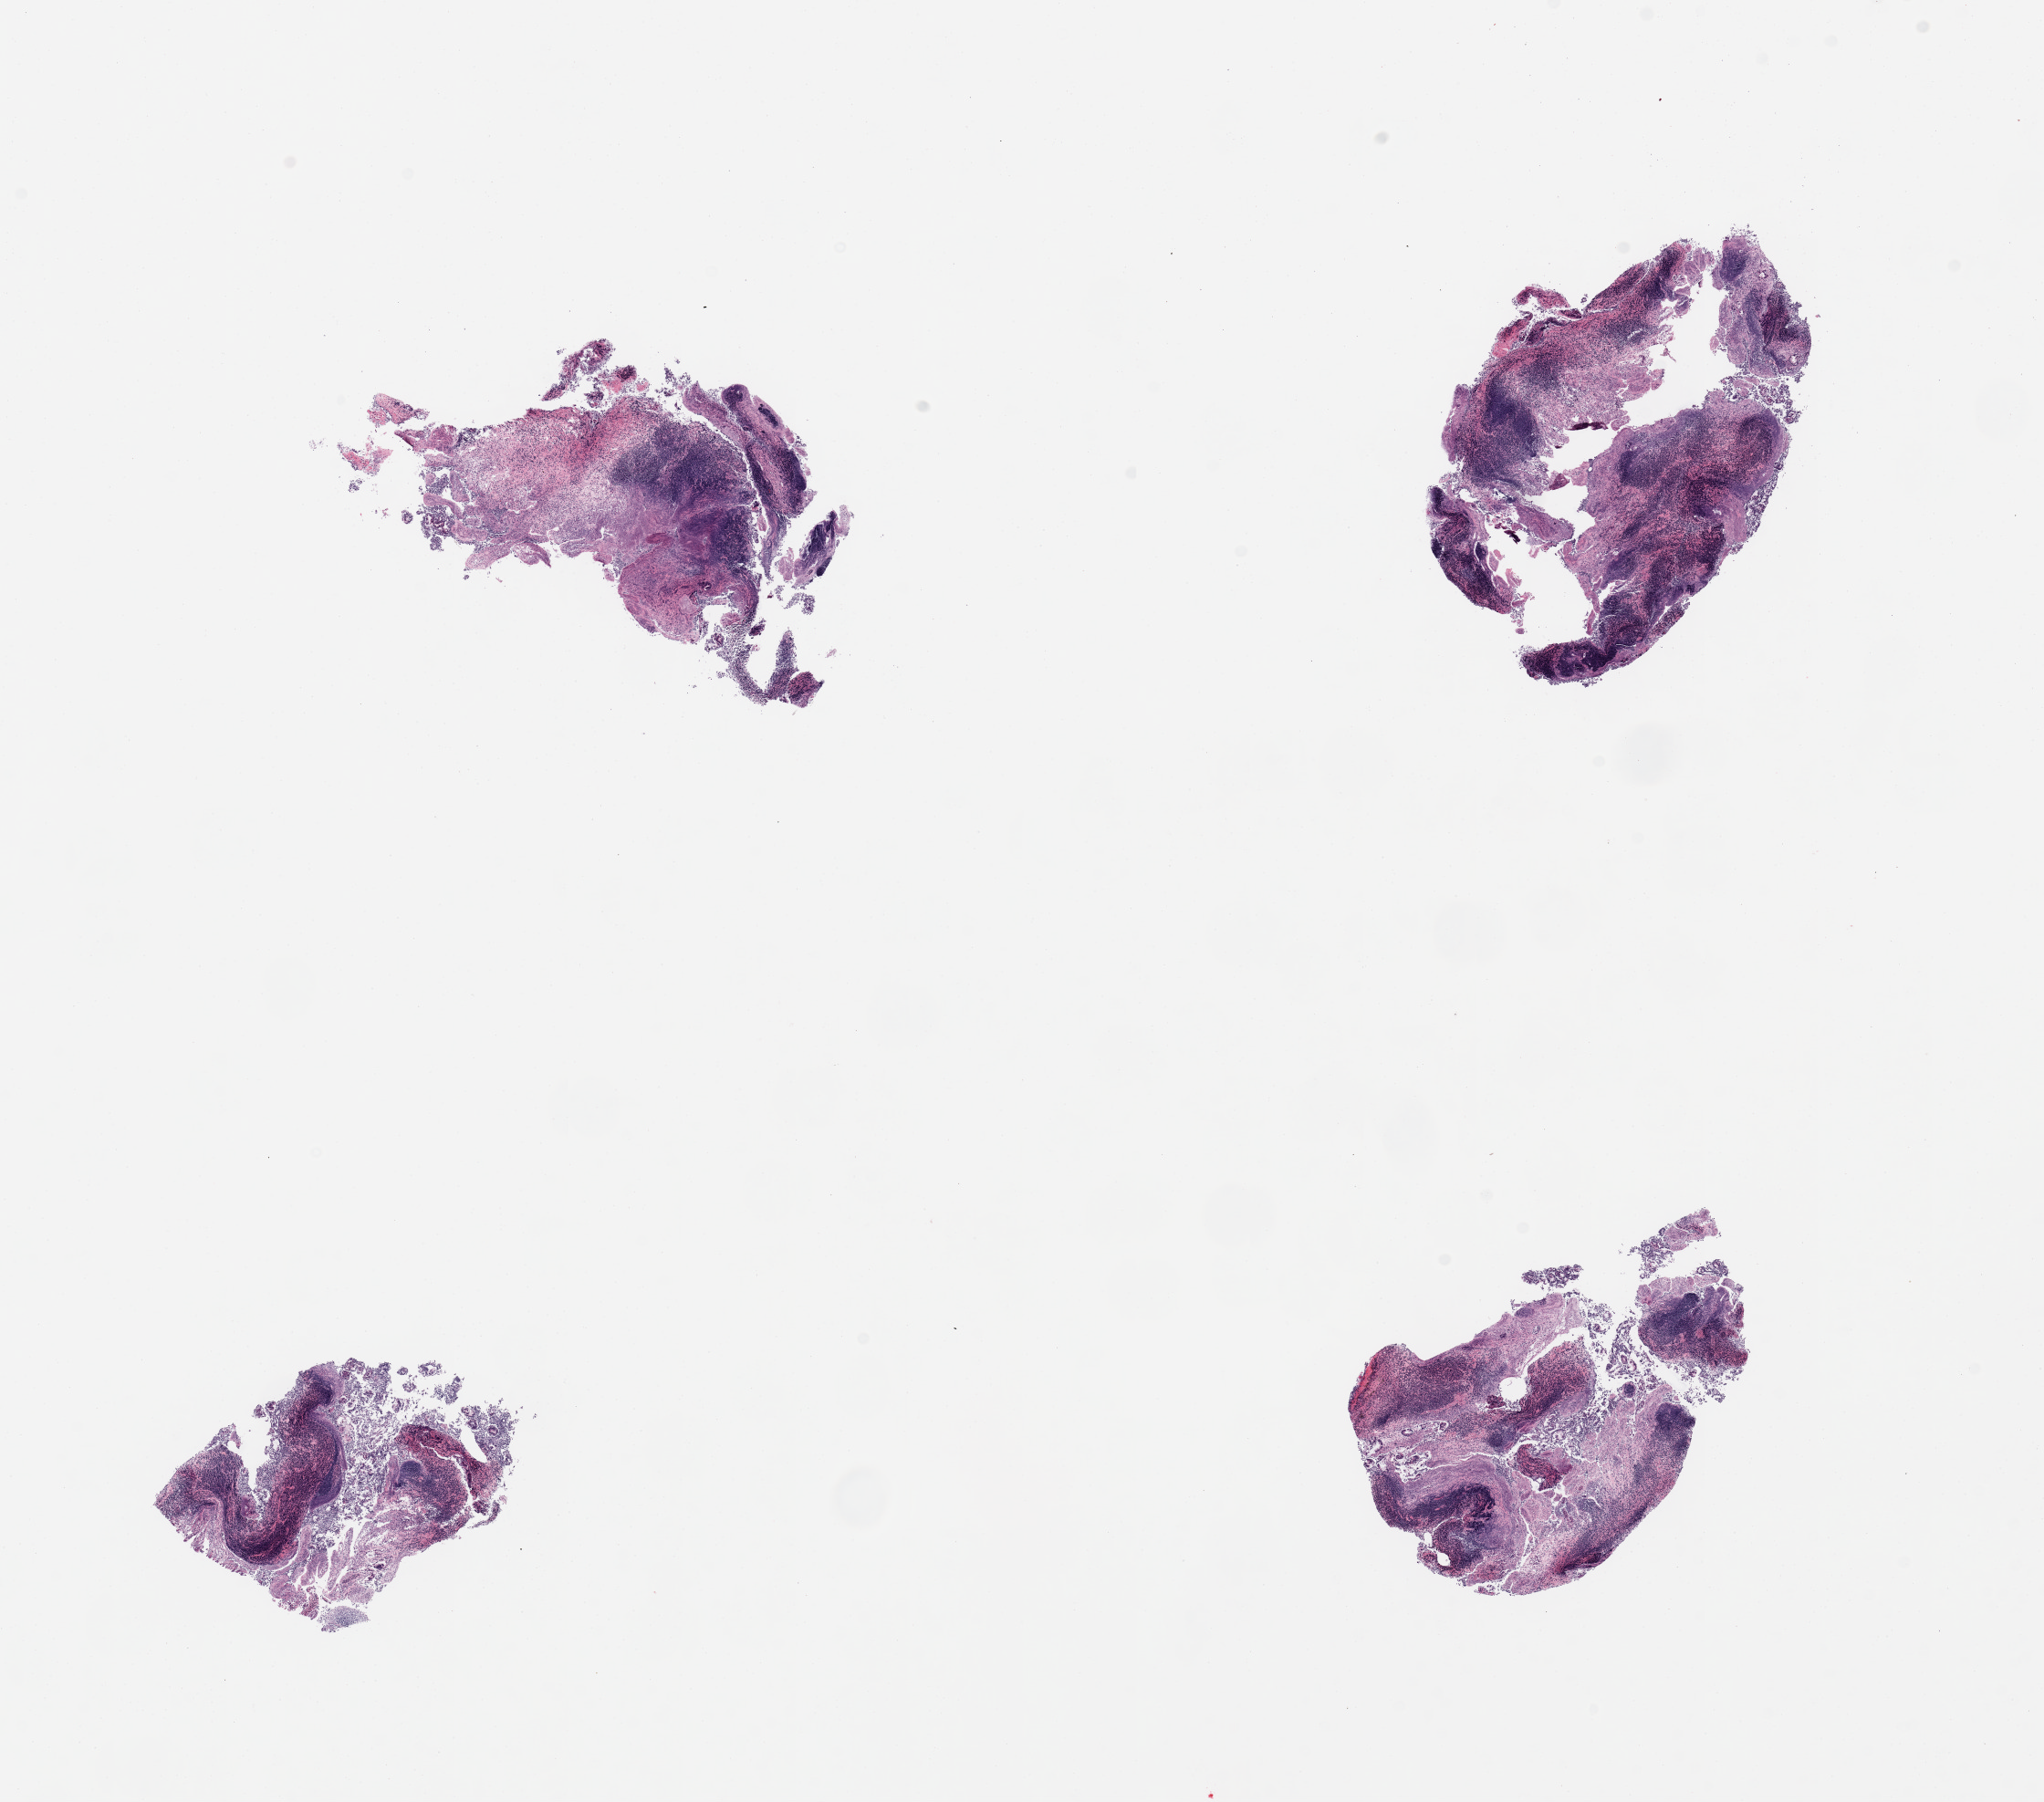
Digitized haematoxylin and eosin-stained section — a low-resolution overview of the entire scanned area, about 17.7 x 15.6 mm; PAXgene-fixed, paraffin-embedded tissue; section of ileum (target tissue); tissue donor sample. Donor: female.
Reviewer comment on this tissue sample: 4 piecesm glandular mucosa sloughed; residual lymphoid elements ~30% of tissue.